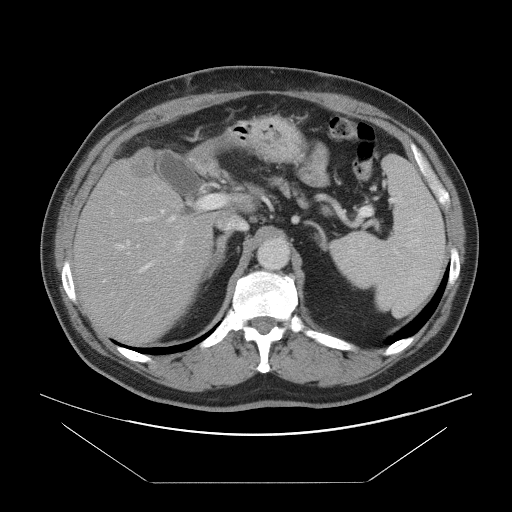
Contrast-enhanced abdominal CT, one axial slice; slice 57 of 97 in the series (ordered by position); 120 kVp; soft-tissue window (W 400 / L 40 HU); 5 mm slice thickness; 512 × 512 image matrix, field of view 442 × 442 mm. Male patient, age 62 years. Case-level facts recorded for this patient, not image findings: diagnosis: colorectal cancer liver metastases, imaged before liver resection; multiple liver metastases: no; largest metastasis: 7 cm; disease in both lobes: yes.
Structures marked on this image (manually delineated by an expert):
- hepatic veins: box from (x=116, y=186) to (x=165, y=255) px
- liver: (x=75, y=150)–(x=216, y=343)
- planned liver remnant (the part of the liver to remain after resection): (x=75, y=177)–(x=217, y=343)
- portal vein (with intrahepatic branches): (x=133, y=194)–(x=227, y=272)
- liver metastasis: (x=130, y=152)–(x=153, y=180)